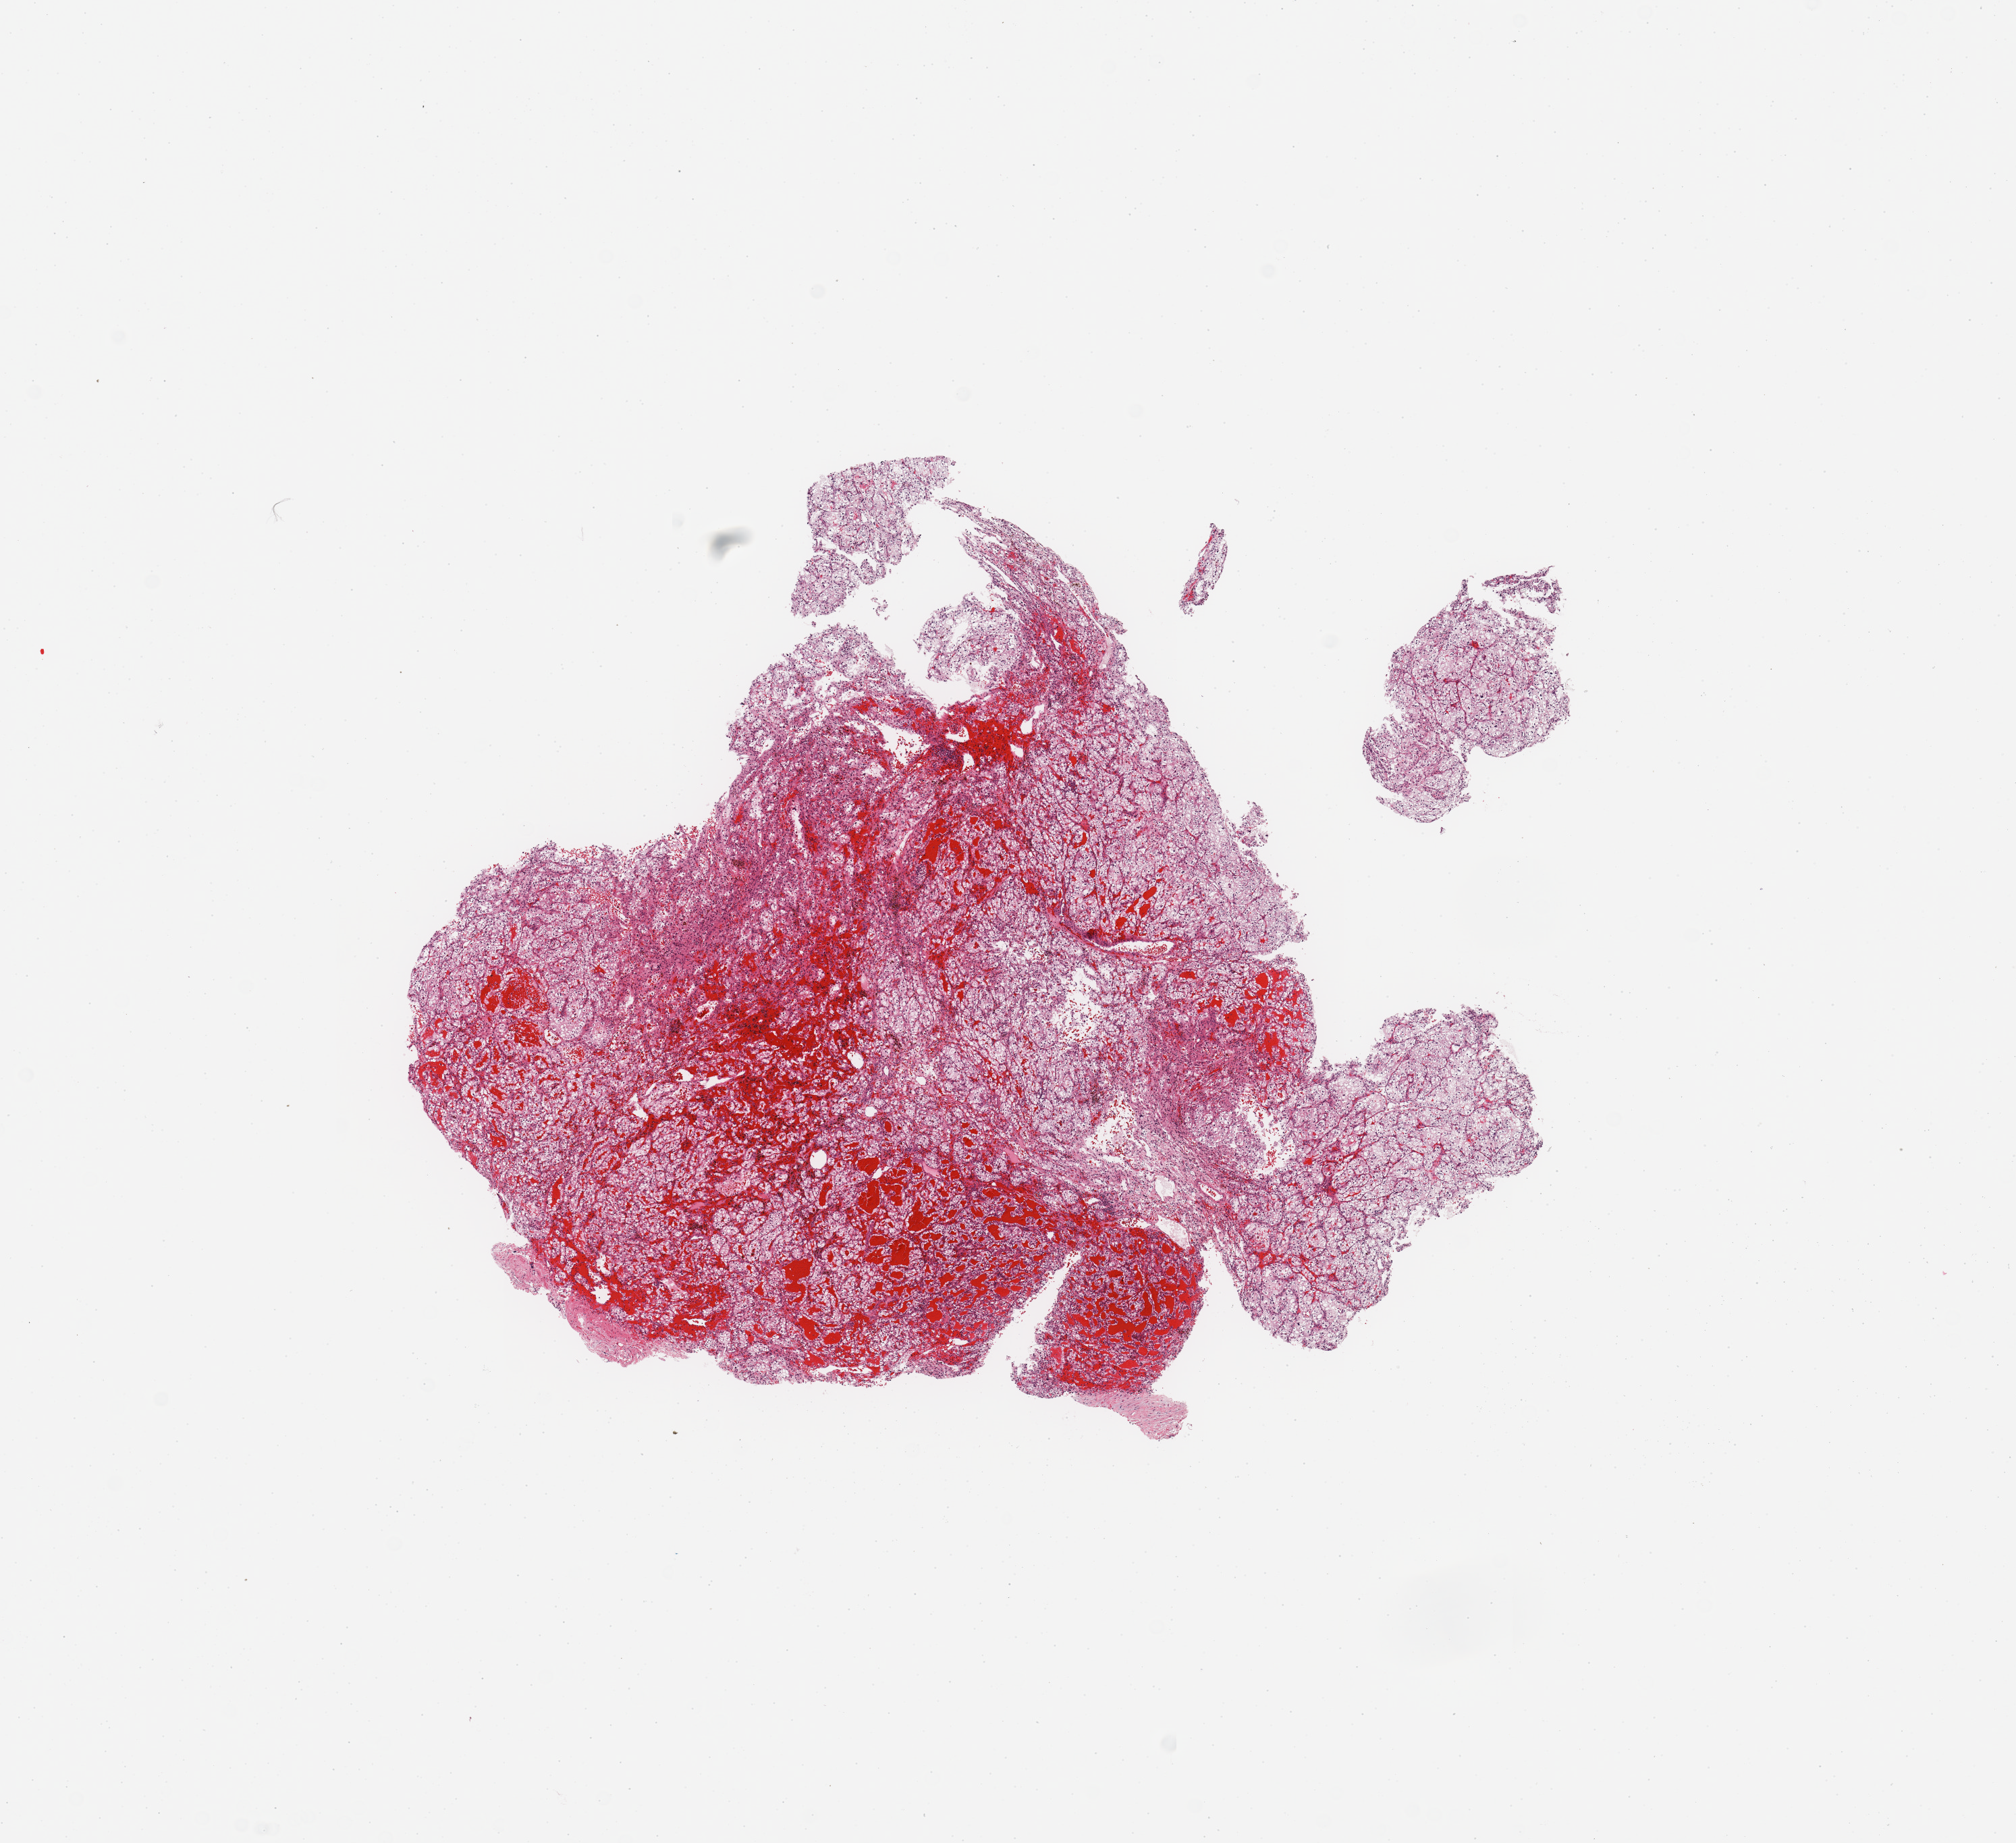
Whole-slide histology image, H&E-stained — shown as a low-resolution overview of the whole scanned area (about 11.8 x 10.8 mm). Kidney, tumour tissue. 85-year-old male patient. Histologic grade: G2 (moderately differentiated).
Primary tumour site (as recorded): lower pole. Histologic diagnosis: Renal cell carcinoma, NOS. AJCC pathologic stage: III.